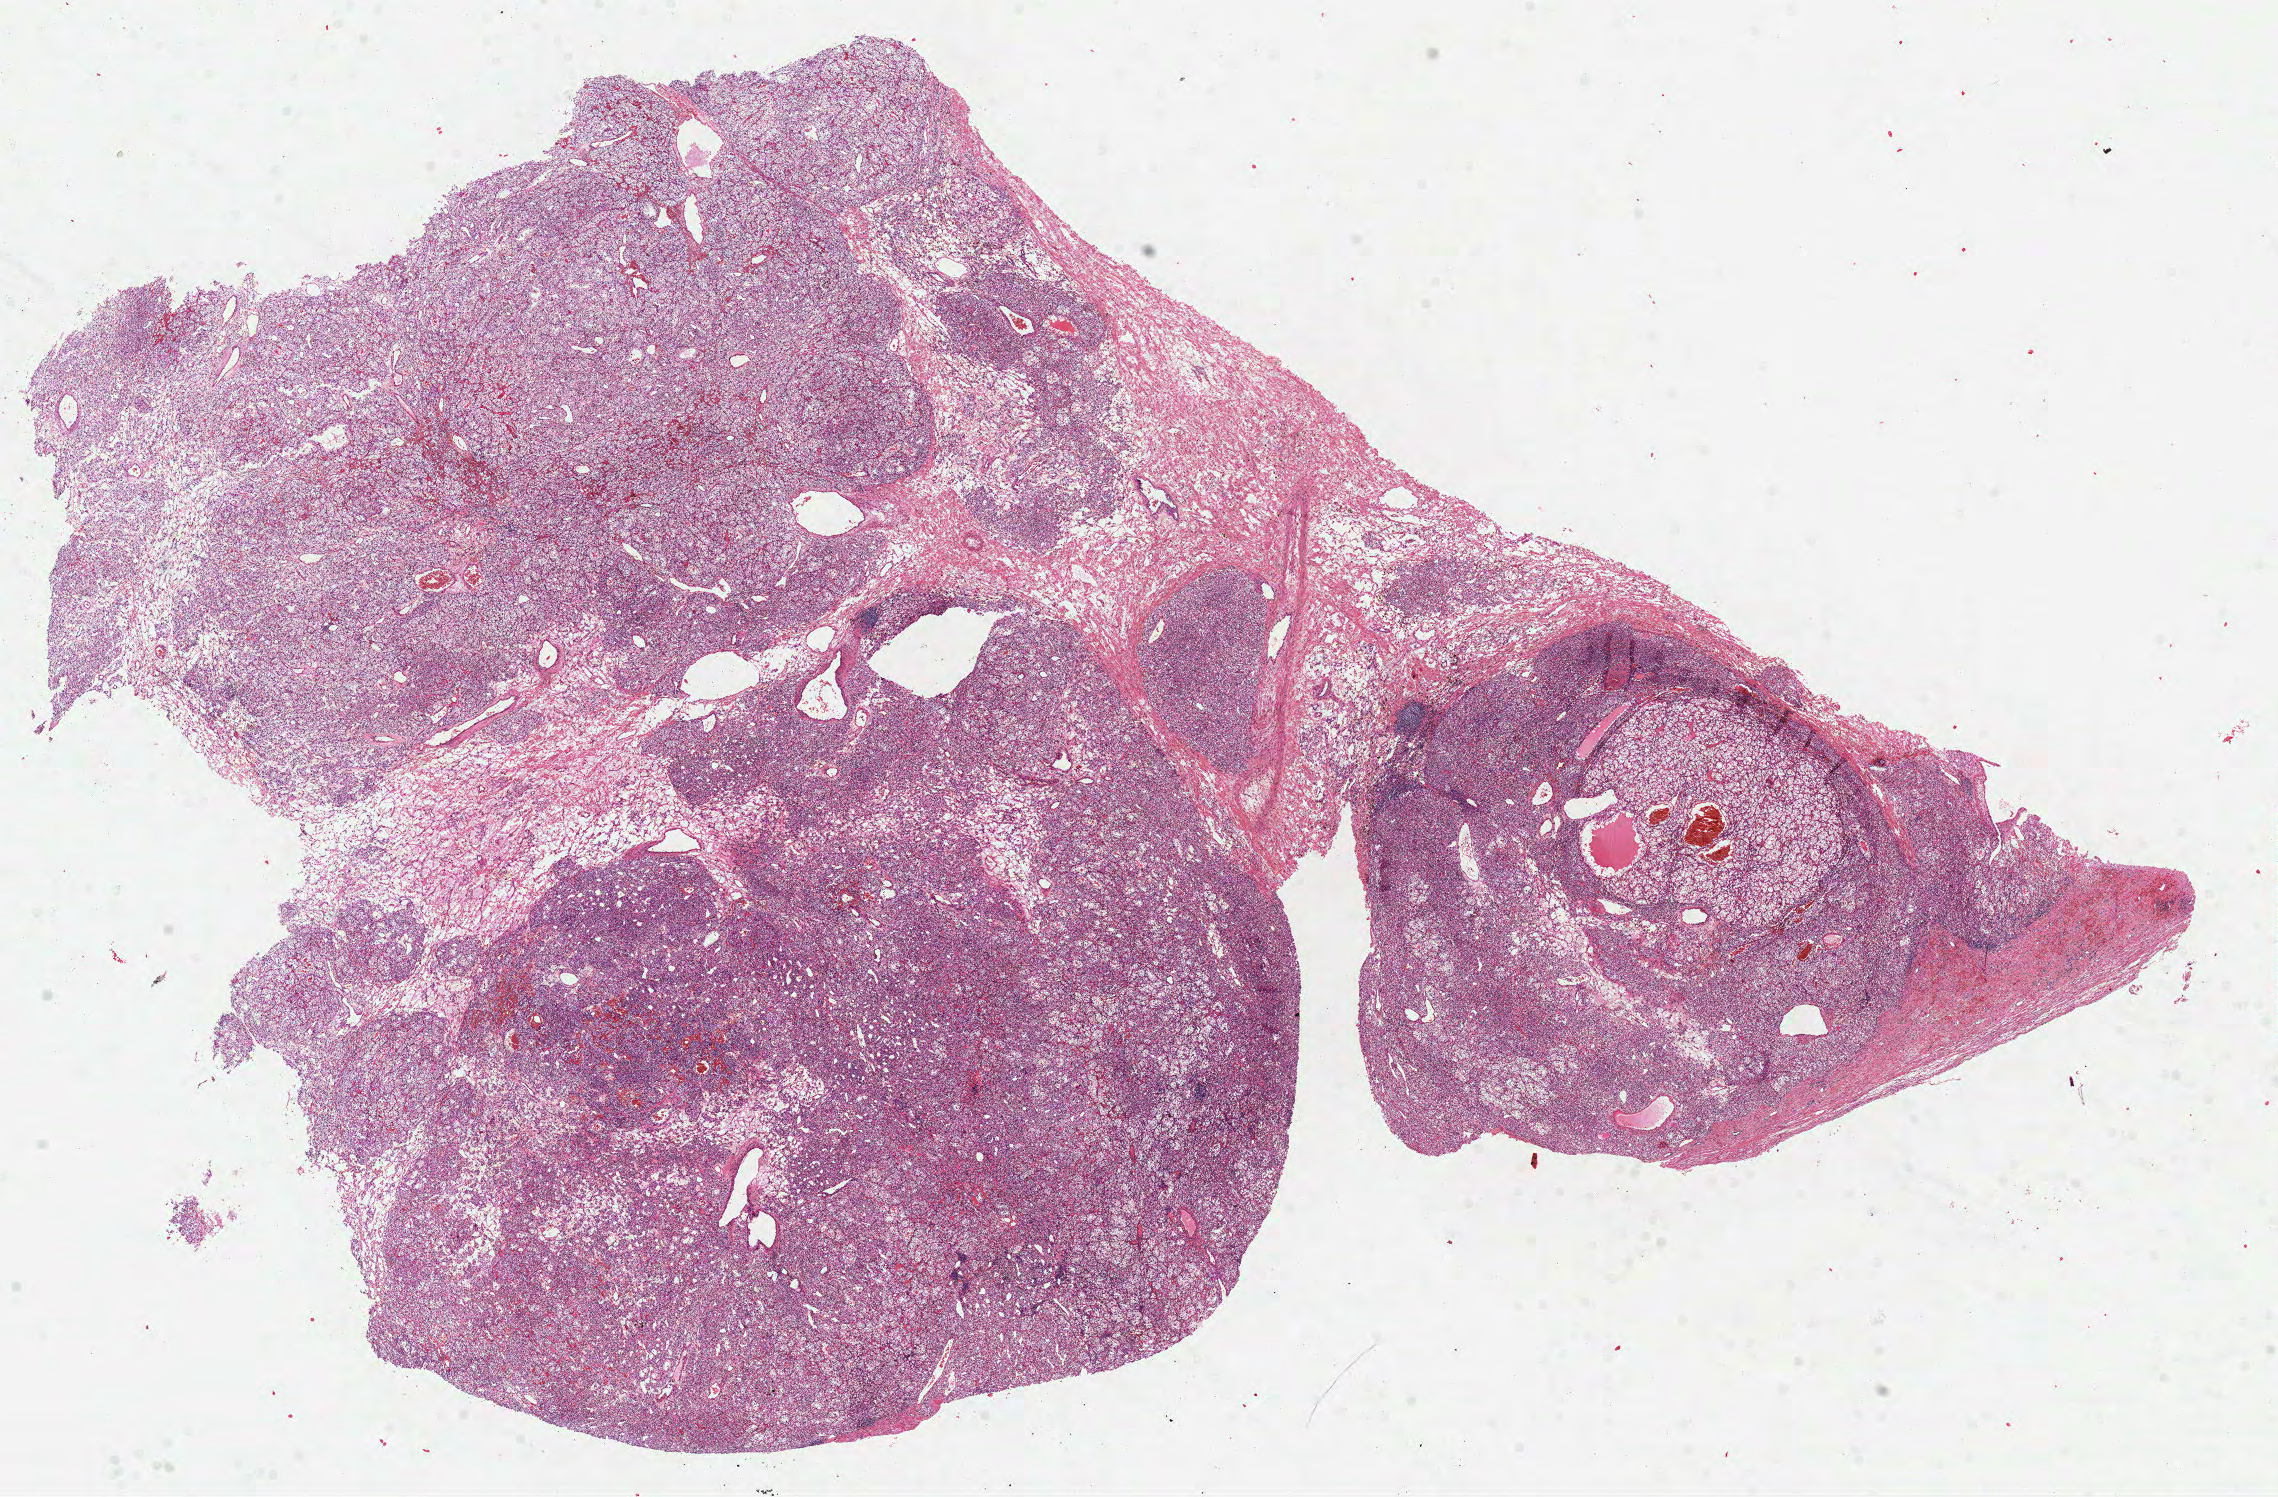
H&E-stained whole-slide image, a low-resolution overview of the entire scanned area, about 18.4 x 12.1 mm (acquisition: 40x scan), formalin-fixed paraffin-embedded (FFPE) diagnostic section, primary tumour sample from the kidney. Female, age 68 years at initial diagnosis. Histologic grade: G3 (poorly differentiated).
- AJCC pathologic stage: IV (7th edition)
- pathologic diagnosis: Clear cell adenocarcinoma, NOS